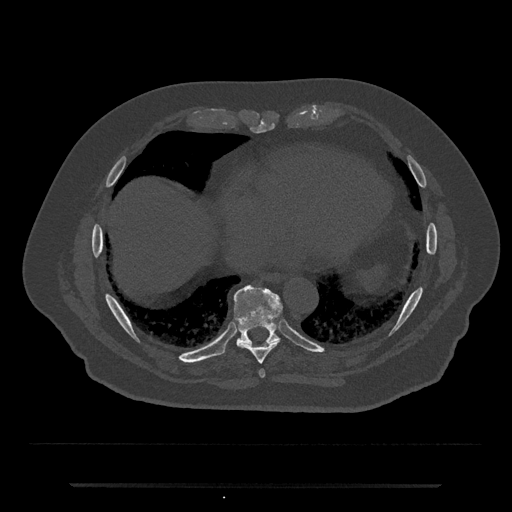
CT including the spine, one axial slice. Position 784 of 797 along the scan axis. Reconstruction kernel Br40s/3. Bone window (W 1800 / L 400 HU). 0.5 mm slice thickness. 512 × 512 image matrix. Male patient, age 80 years. Case-level facts recorded for this patient, not image findings: primary cancer: prostate.
Annotated regions visible in this slice (semi-automatically segmented with operator editing):
- T8 vertebra: box from (x=237, y=327) to (x=279, y=364) px
- T9 vertebra: (x=219, y=286)–(x=282, y=354)